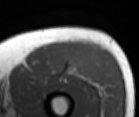
MRI of an extremity soft-tissue mass, one axial slice. Position 41 of 86 along the scan axis. MR volume resampled by the dataset authors to the PET/CT grid (not the native acquisition matrix). 139 × 117 image matrix, field of view 136 × 114 mm. Male patient. Case-level facts recorded for this patient, not image findings: histological type: extraskeletal osteosarcoma; grade: high; site of the primary tumour: thigh.
Structures marked on this image (expert contour drawn on MRI and transferred to this co-registered scan by the dataset authors):
- gross tumour volume (mass): bounding box <58,46,94,76> (left, top, right, bottom; pixels)